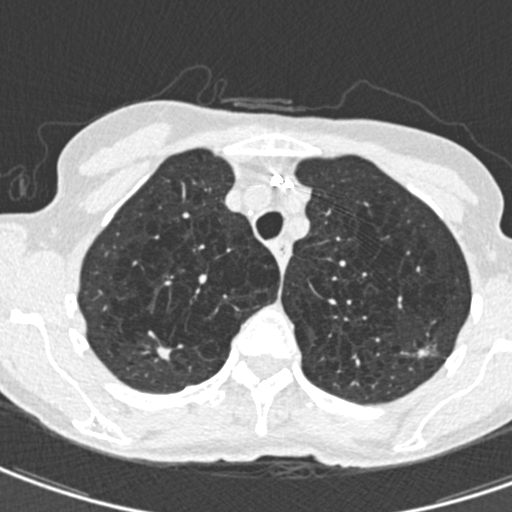
Chest CT (low-dose screening protocol), one axial image. Second screening round (one year after baseline). Lung window (W 1500 / L -600 HU). 0.75 mm slice thickness. 512 × 512 image matrix, field of view 272 × 272 mm. Female participant, aged 71 years at enrolment. Current smoker at enrolment.
Lesion marked by an expert reader, bounding box [x1, y1, x2, y2] px = [405, 332, 445, 370]. The screening reader recorded 2 non-calcified nodules or masses ≥4 mm on this exam (right upper lobe, left upper lobe); which of them this box marks is not recorded. Participant outcome: lung cancer diagnosed 604 days after this screen (after the third annual screen) — adenocarcinoma, NOS, left upper lobe, moderately differentiated (G2), stage IA (AJCC 6th edition), 12 mm at pathology.